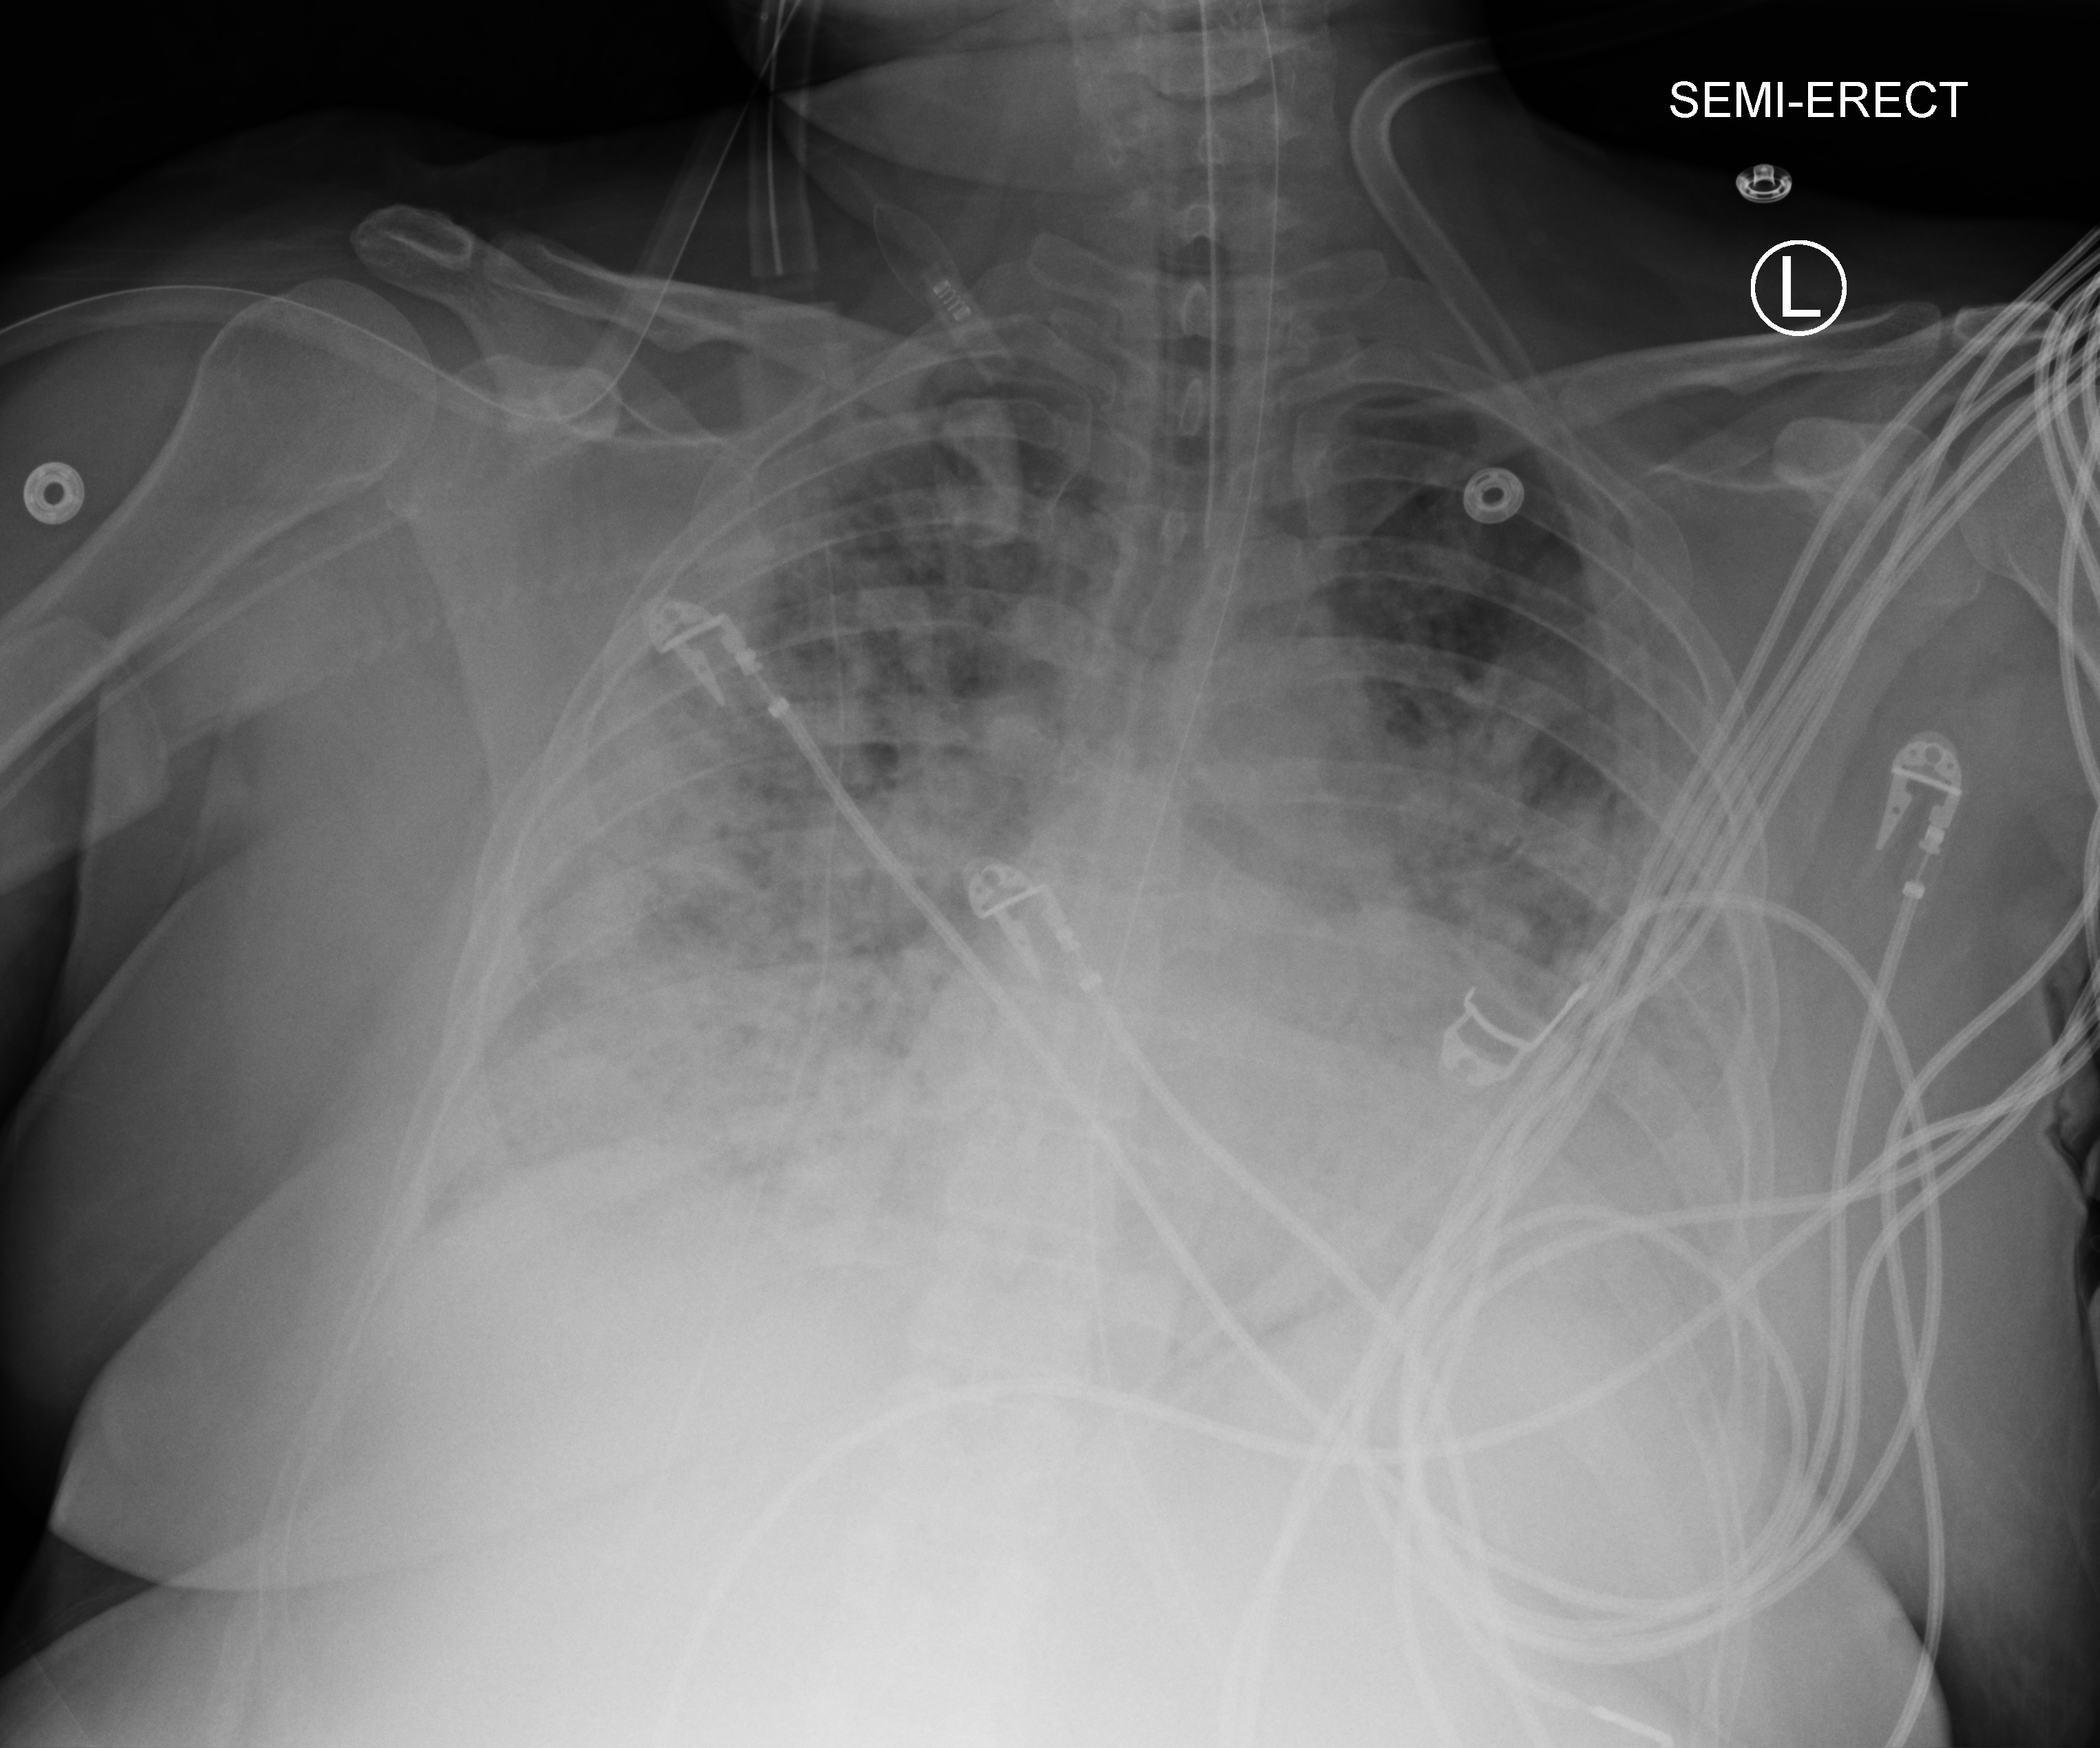
Portable chest radiograph, anteroposterior (AP) projection. Female patient hospitalised with COVID-19, age 18–59 years.
Admission-level facts for this patient (not findings on this image; timing relative to this image not recorded):
- diabetes (admission record): yes
- mechanically ventilated during this hospital stay: yes